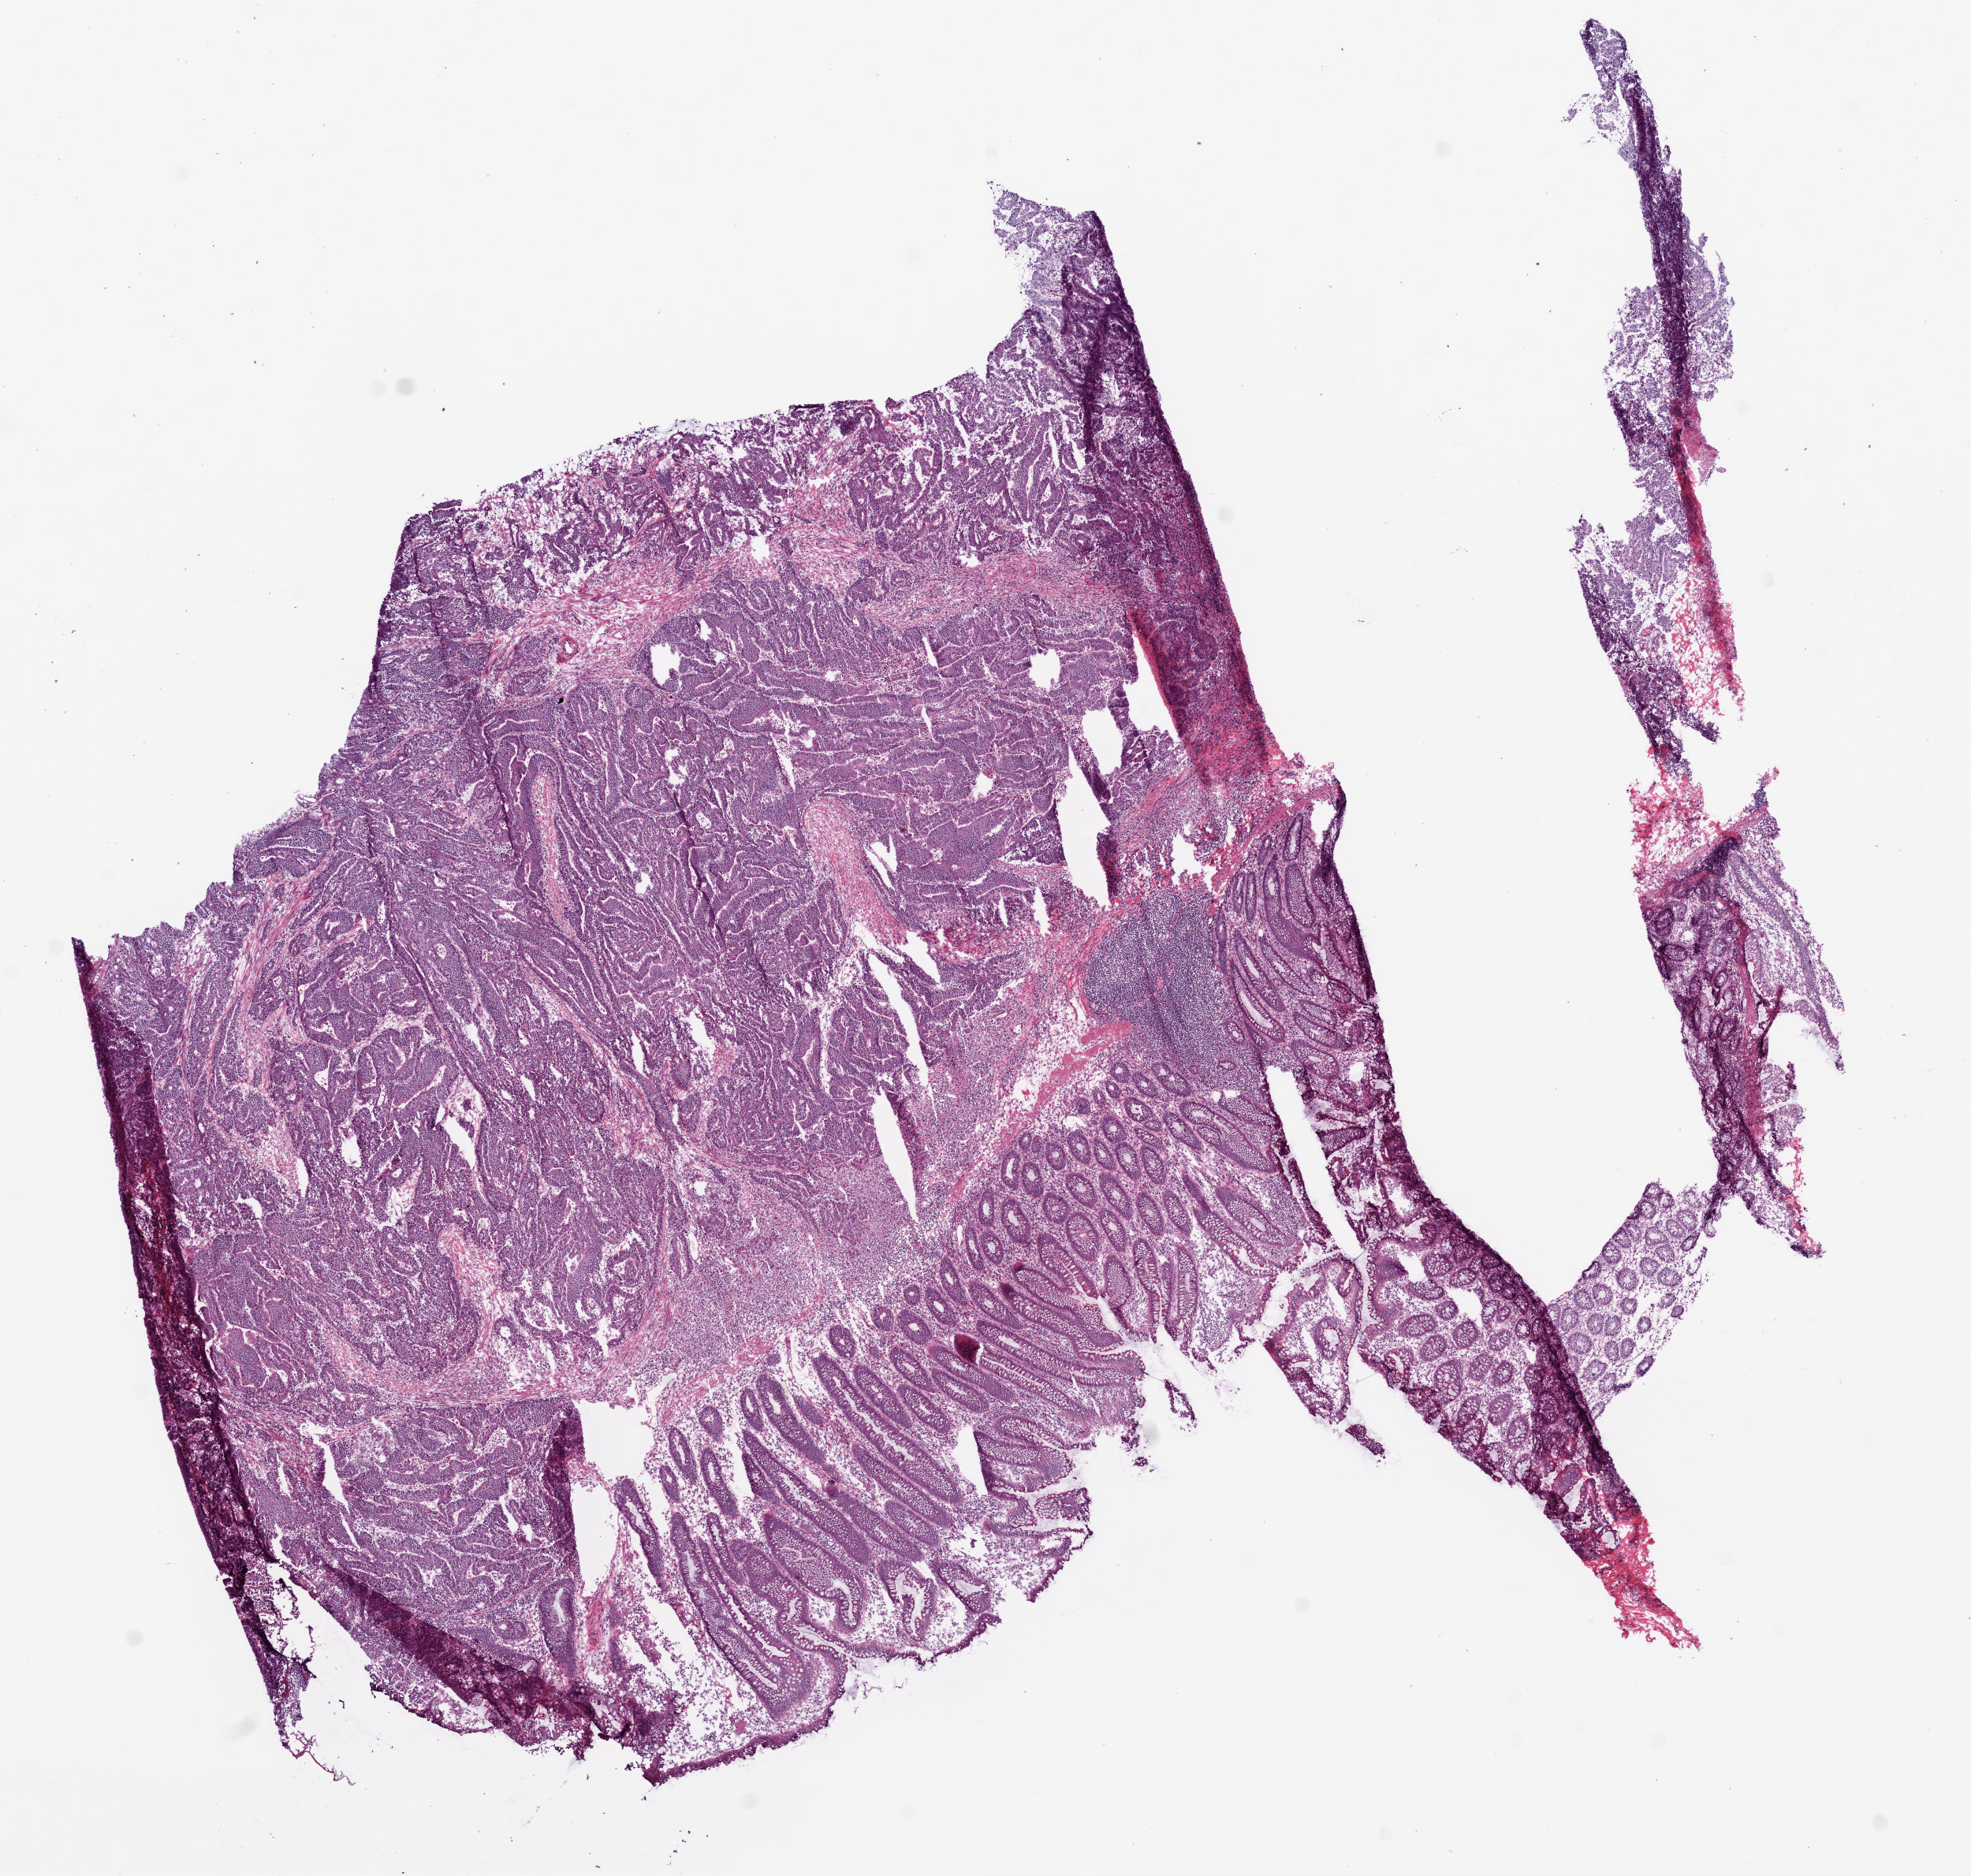
Whole-slide histology image, H&E-stained — shown as a low-resolution overview of the whole scanned area (about 10.0 x 9.5 mm, acquisition: 20x scan), frozen section, primary tumour sample from the colon. Male patient; age at initial diagnosis 68 years. Pathologist review of this section (percent, as recorded): tumour cells 80%, tumour nuclei 80%, normal cells 19%, necrosis 1%. Infiltration values recorded for this section: lymphocyte infiltration 1%, neutrophil infiltration 3%.
- lymph nodes positive (case pathology): 0 of 15 examined
- AJCC pathologic stage: IV
- diagnosis: Adenocarcinoma, NOS